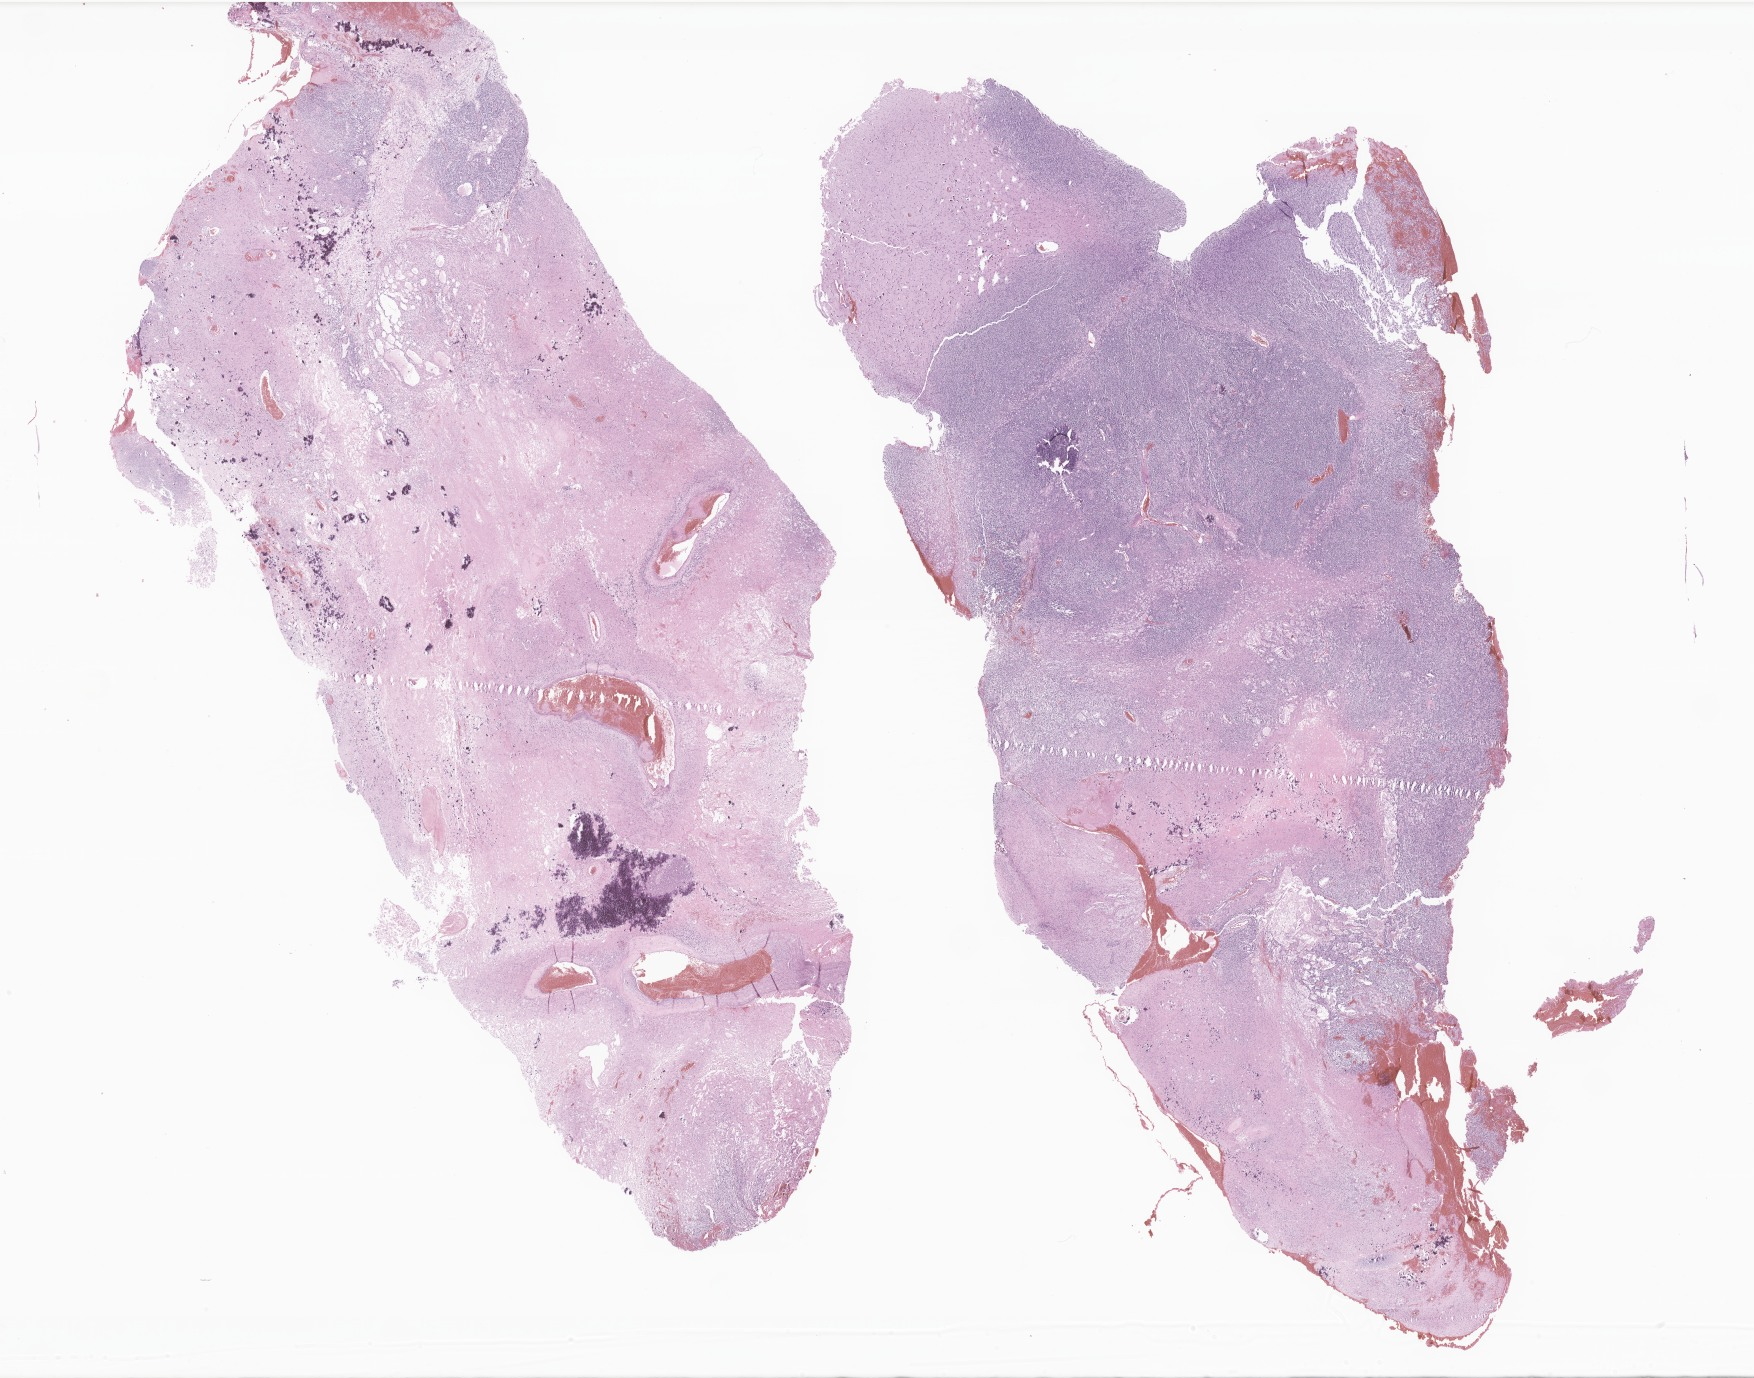
Digitized hematoxylin and eosin (H&E)-stained section of tumor tissue from the brain — a low-resolution overview of the entire scanned area, about 29.6 x 23.2 mm. FFPE section. Patient male; age 131 months (10 years 11 months).
Recorded diagnosis: Astrocytoma, anaplastic, NOS.